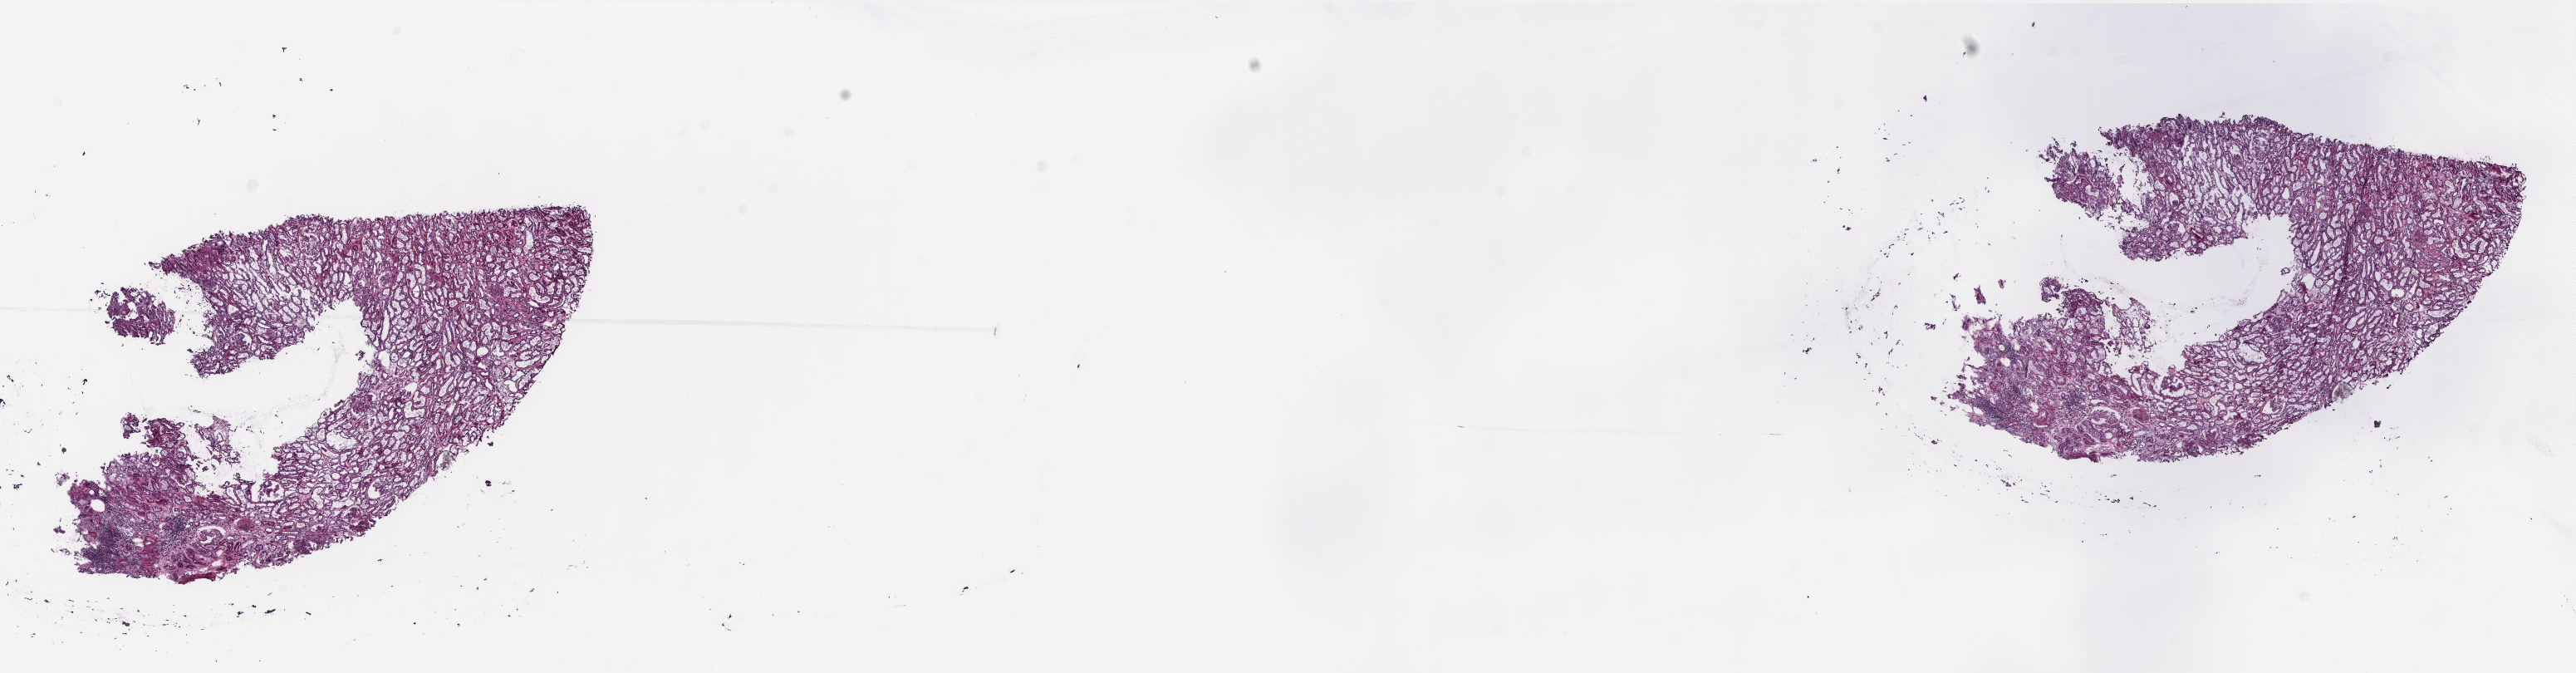
H&E whole-slide image, low-resolution overview of the scanned area, about 25.0 x 6.5 mm, frozen section from the top of the tissue portion, sample: solid tissue normal (non-tumour tissue), kidney. Patient sex: male. Slide review estimates, as recorded: tumour cells 0%, tumour nuclei 0%.
This section: solid tissue normal sample (biorepository sample class). Patient diagnosis: Papillary adenocarcinoma, NOS.